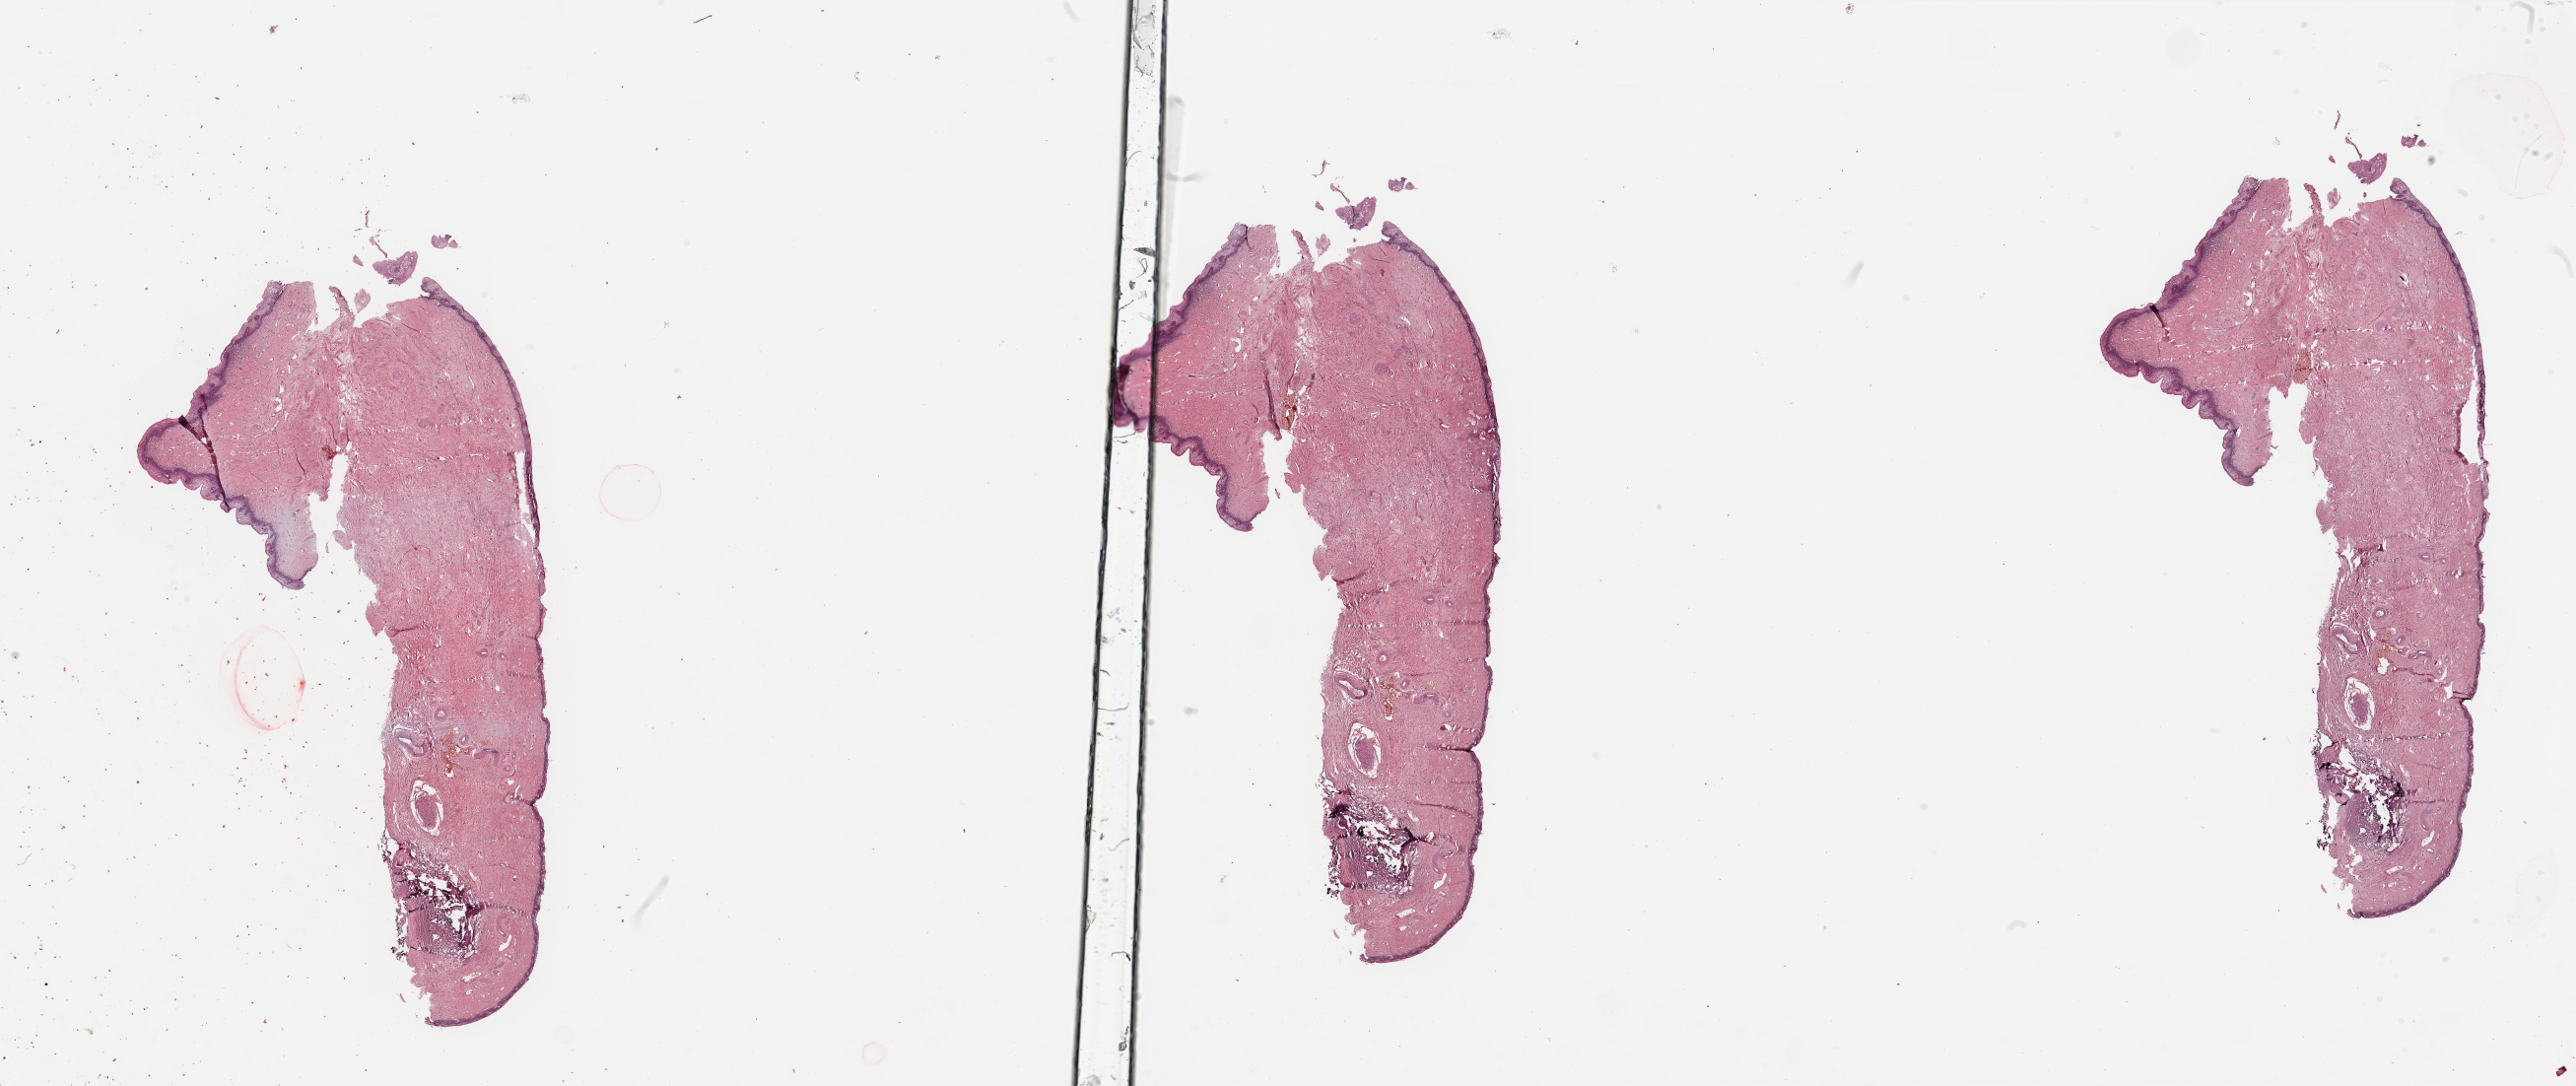
H&E whole-slide image — low-resolution overview of the scanned area, about 41.3 x 17.4 mm, normal (non-tumour) tissue sample, uterus. 54-year-old female patient.
This section: normal (non-tumour) tissue from the same patient. Patient diagnosis: Endometrioid adenocarcinoma, NOS.